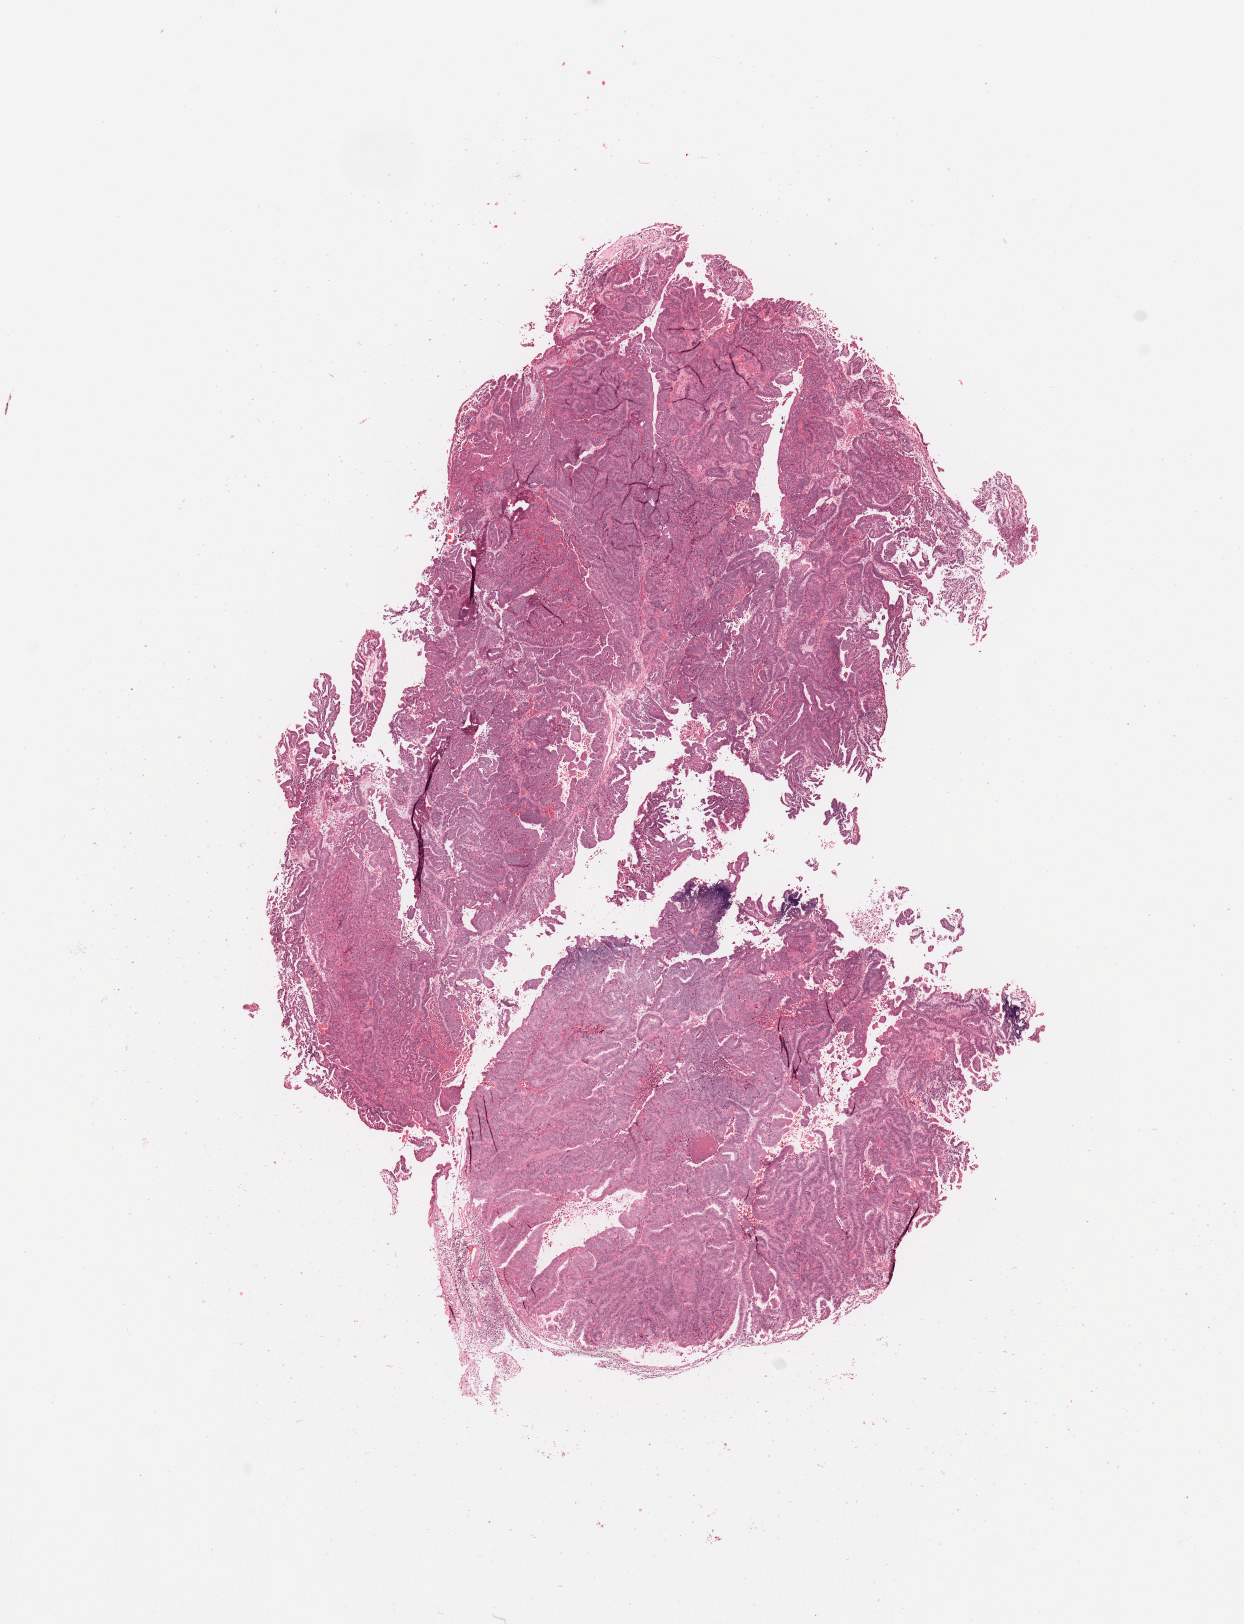
Hematoxylin and eosin (H&E) stained whole-slide image — low-resolution overview of the scanned area, about 9.8 x 12.9 mm (slide scanned at 20x). Tumour tissue sample, sampled site: uterus. Female, 81 y/o. Histologic grade: G2 (moderately differentiated). Composition of this section per pathologist review: tumour nuclei 90%, necrosis 2%.
- AJCC pathologic stage: I
- diagnosis: Endometrioid adenocarcinoma, NOS